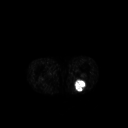
FDG PET of an extremity soft-tissue mass (from a PET/CT study), one axial slice; slice 197 of 267 in the series (ordered by position); 3.27 mm slice thickness; 128 × 128 image matrix, field of view 500 × 500 mm. Male patient, age 54 years. From the clinical record (not read from this slice): histological type: synovial sarcoma; site of the primary tumour: left poplietal fossa.
Outlined on this slice (expert contour drawn on MRI and transferred to this co-registered scan by the dataset authors):
- gross tumour volume (mass): bounding box [x1, y1, x2, y2] px = [74, 79, 87, 92]